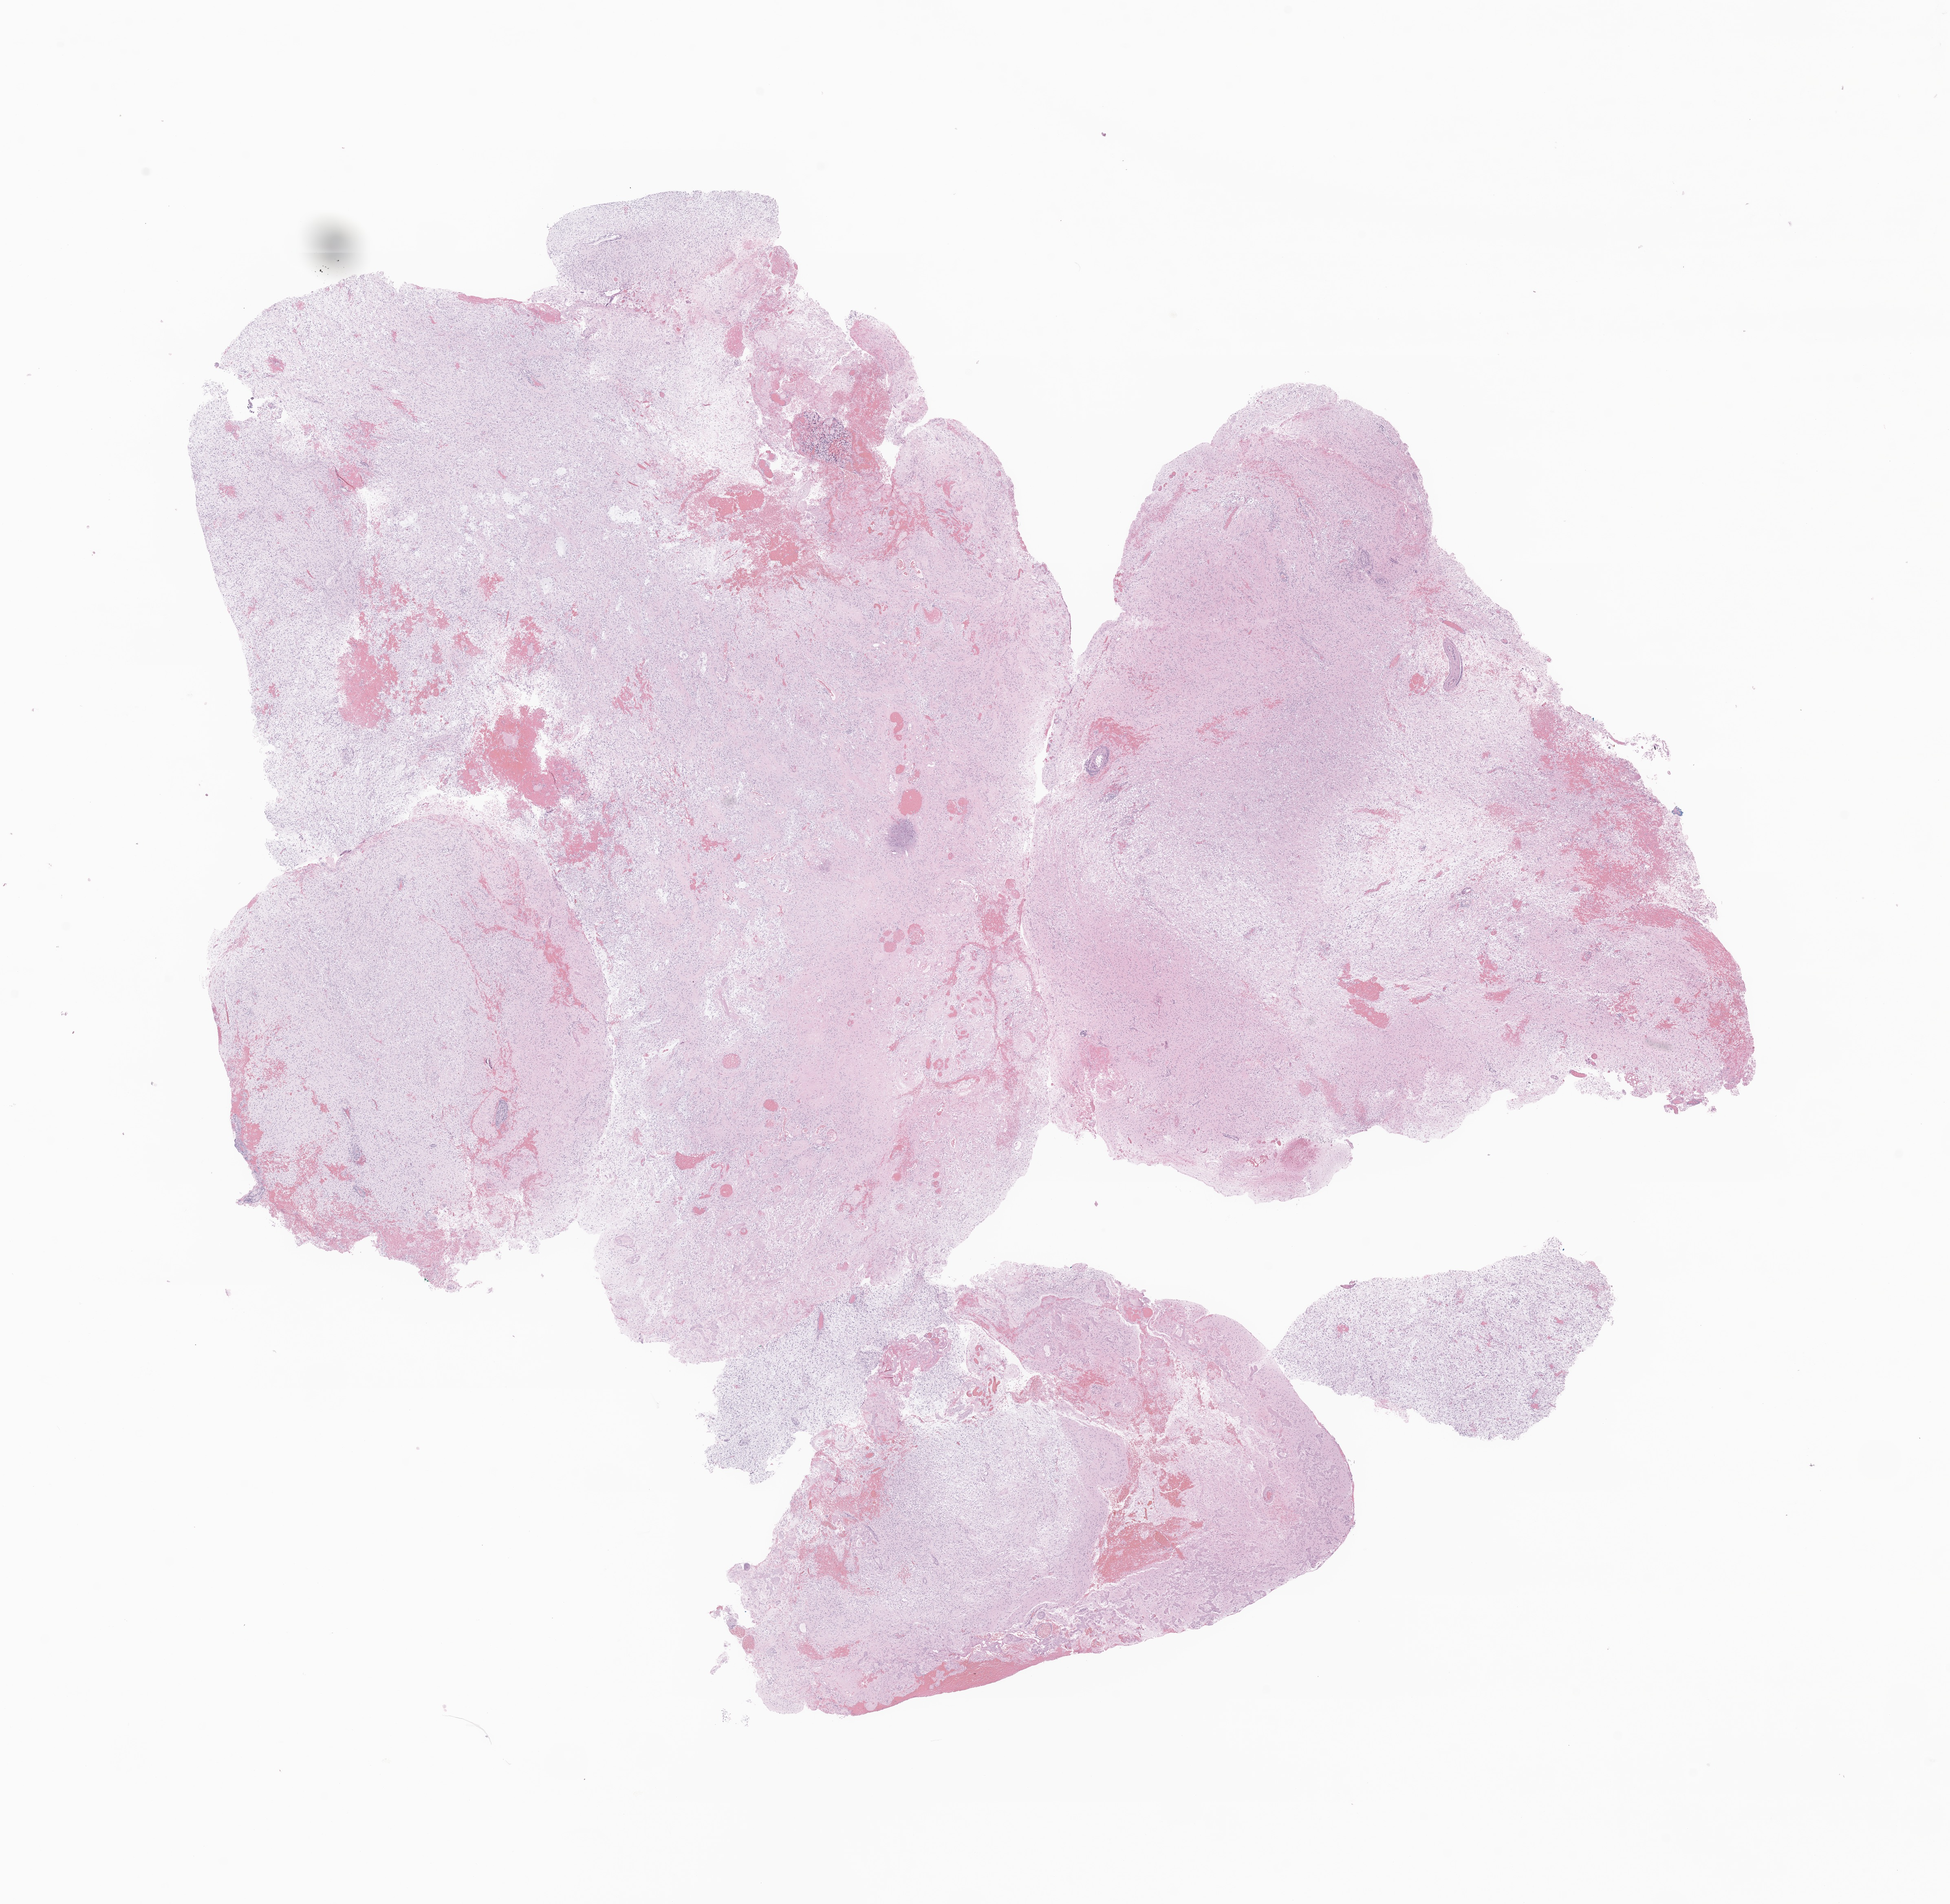
Whole-slide image, haematoxylin and eosin stain of tumor tissue from the cerebellum — a low-resolution overview of the entire scanned area, about 20.2 x 19.7 mm. FFPE section. Male patient, age 181 months (15 years 1 month).
* diagnosis (ICD-O-3 morphology term): Pilocytic astrocytoma